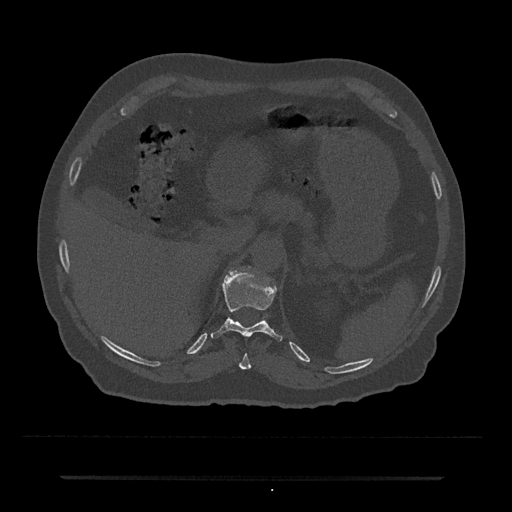
CT including the spine, one axial slice. Slice 180 of 797 in the series (ordered by position). Reconstruction kernel Br40s/3. 120 kVp. Bone window (W 1800 / L 400 HU). 0.5 mm slice thickness. 512 × 512 image matrix. Patient: male, 69 years. Case-level facts recorded for this patient, not image findings: primary cancer: prostate.
Outlined on this slice (semi-automatically segmented with operator editing):
- T10 vertebra: bounding box (x1, y1, x2, y2) in pixels: (239, 353, 251, 370)
- T11 vertebra: (211, 272, 283, 342)